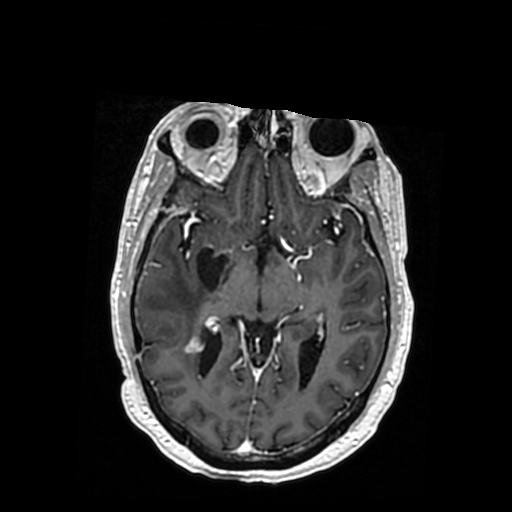
Brain MRI from a brain-tumour surgery series, one axial slice; position 199 of 364 along the scan axis; T1-weighted post-contrast; 512 × 512 image matrix, field of view 260 × 260 mm. Case-level facts recorded for this patient, not image findings: histopathology: Oligodendroglioma; WHO grade: 3; IDH mutation: yes.
Outlined on this slice (outlined manually by an expert reader):
- previous resection cavity: bounding box [x1, y1, x2, y2] px = [196, 248, 228, 289]
- tumour: [188, 336, 206, 348]